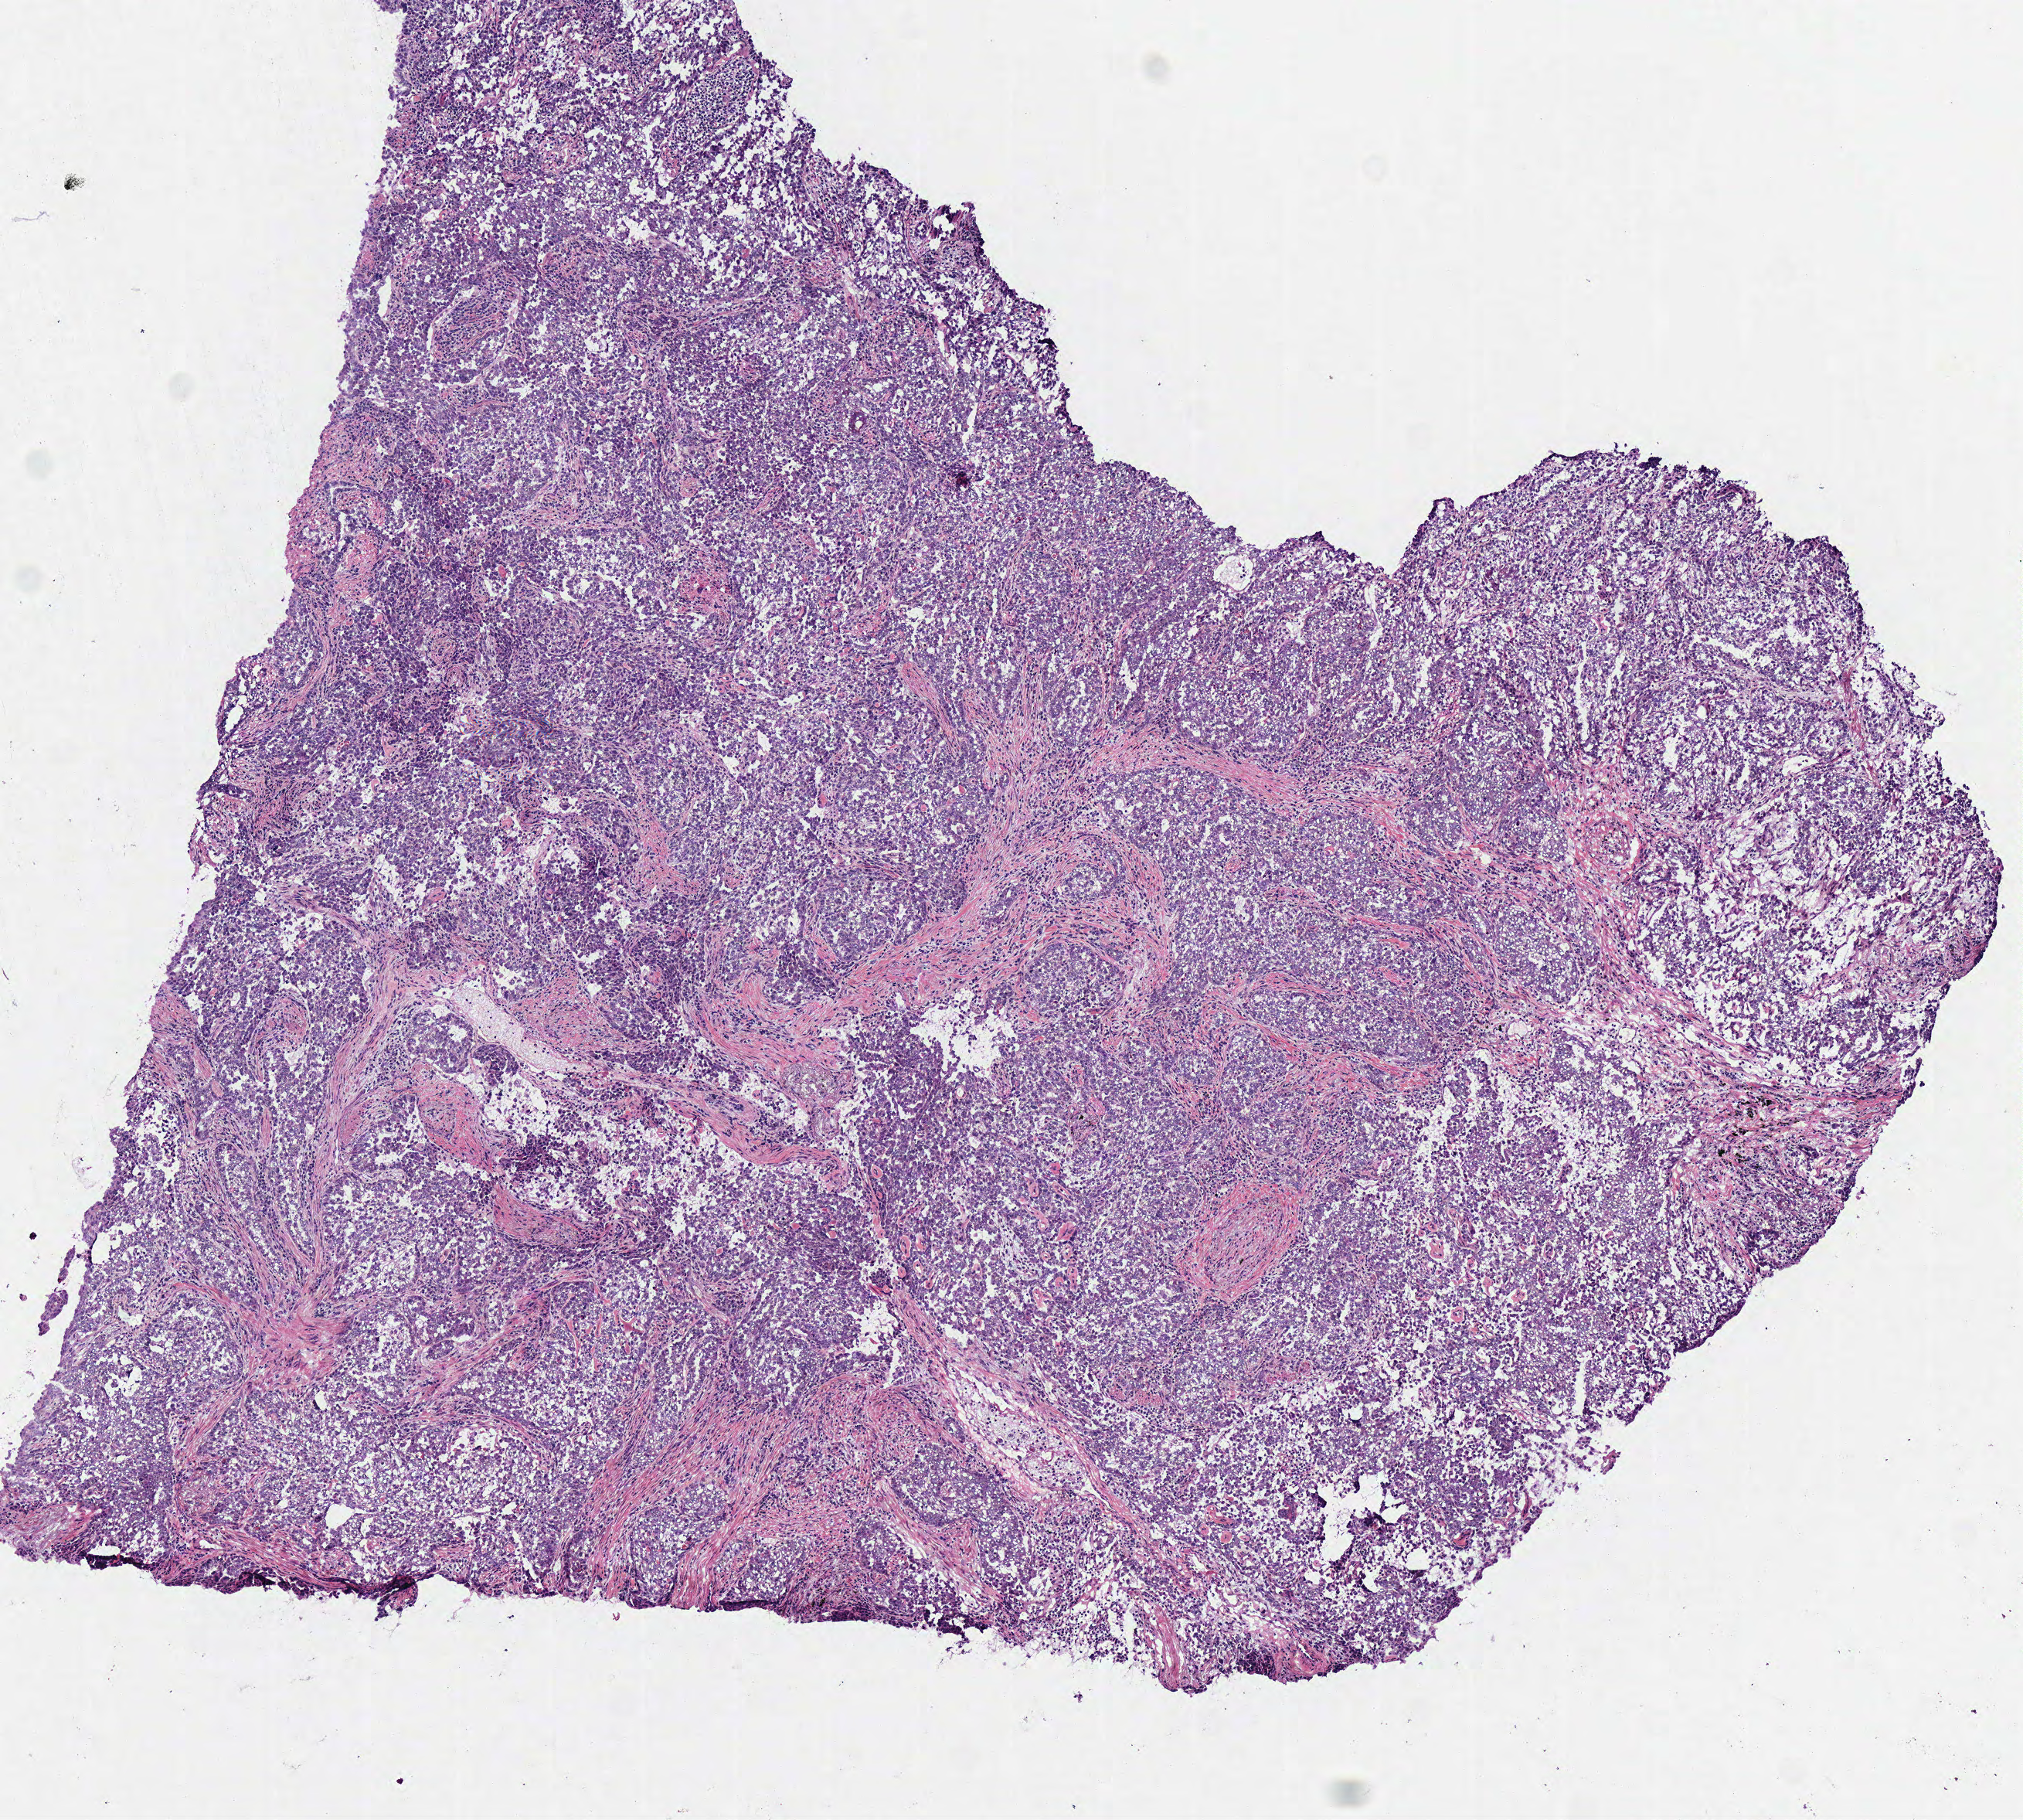
Digitized H&E tissue section (whole slide) — low-resolution overview of the scanned area, about 5.2 x 4.6 mm. Frozen section from the bottom of the tissue portion. Sample: primary tumour, lung. Female, age 59 years at initial diagnosis. Slide review estimates, as recorded: tumour cells 90%, tumour nuclei 80%, normal cells 0%, stromal cells 10%, necrosis 0%.
AJCC pathologic stage: IA (7th edition). Diagnosis: Adenocarcinoma, NOS.